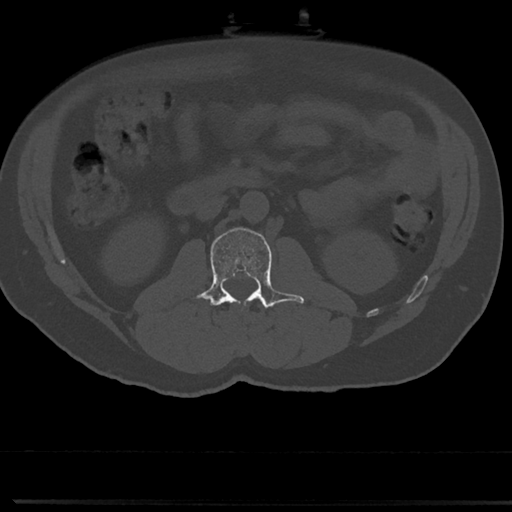
CT including the spine, one axial slice. Position 18 of 817 along the scan axis. Reconstruction kernel Br40s/3. Bone window (W 1800 / L 400 HU). 0.5 mm slice thickness. 512 × 512 image matrix, field of view 355 × 355 mm. Male patient, age 61 years. From the clinical record (not read from this slice): primary cancer: prostate.
Outlined on this slice (semi-automatically segmented with operator editing):
- L1 vertebra: bounding box <259,305,261,307> (left, top, right, bottom; pixels)
- L2 vertebra: <191,227,304,310>